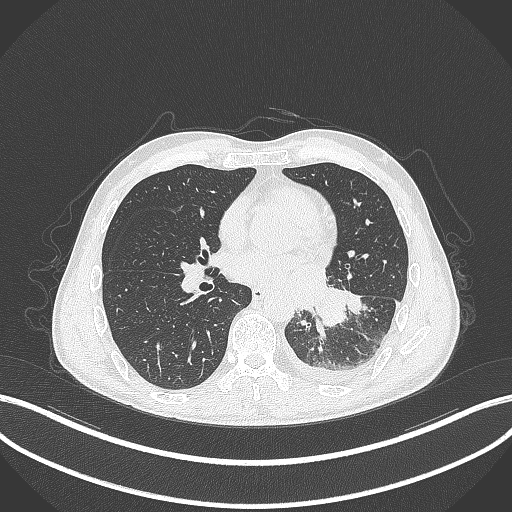
Chest CT, one axial slice; slice 141 of 295 in the series (ordered by position); reconstruction kernel B70f; lung window (W 1500 / L -600 HU); 1 mm slice thickness; 512 × 512 image matrix. Male patient, age 47 years. From the clinical record (not read from this slice): clinical TNM (as recorded): T3 N1 M1c; histopathological grade: G3.
Annotated regions visible in this slice (bounding box drawn by a radiologist):
- lung tumour (recorded histology: small cell carcinoma): bounding box <314,285,349,329> (left, top, right, bottom; pixels)